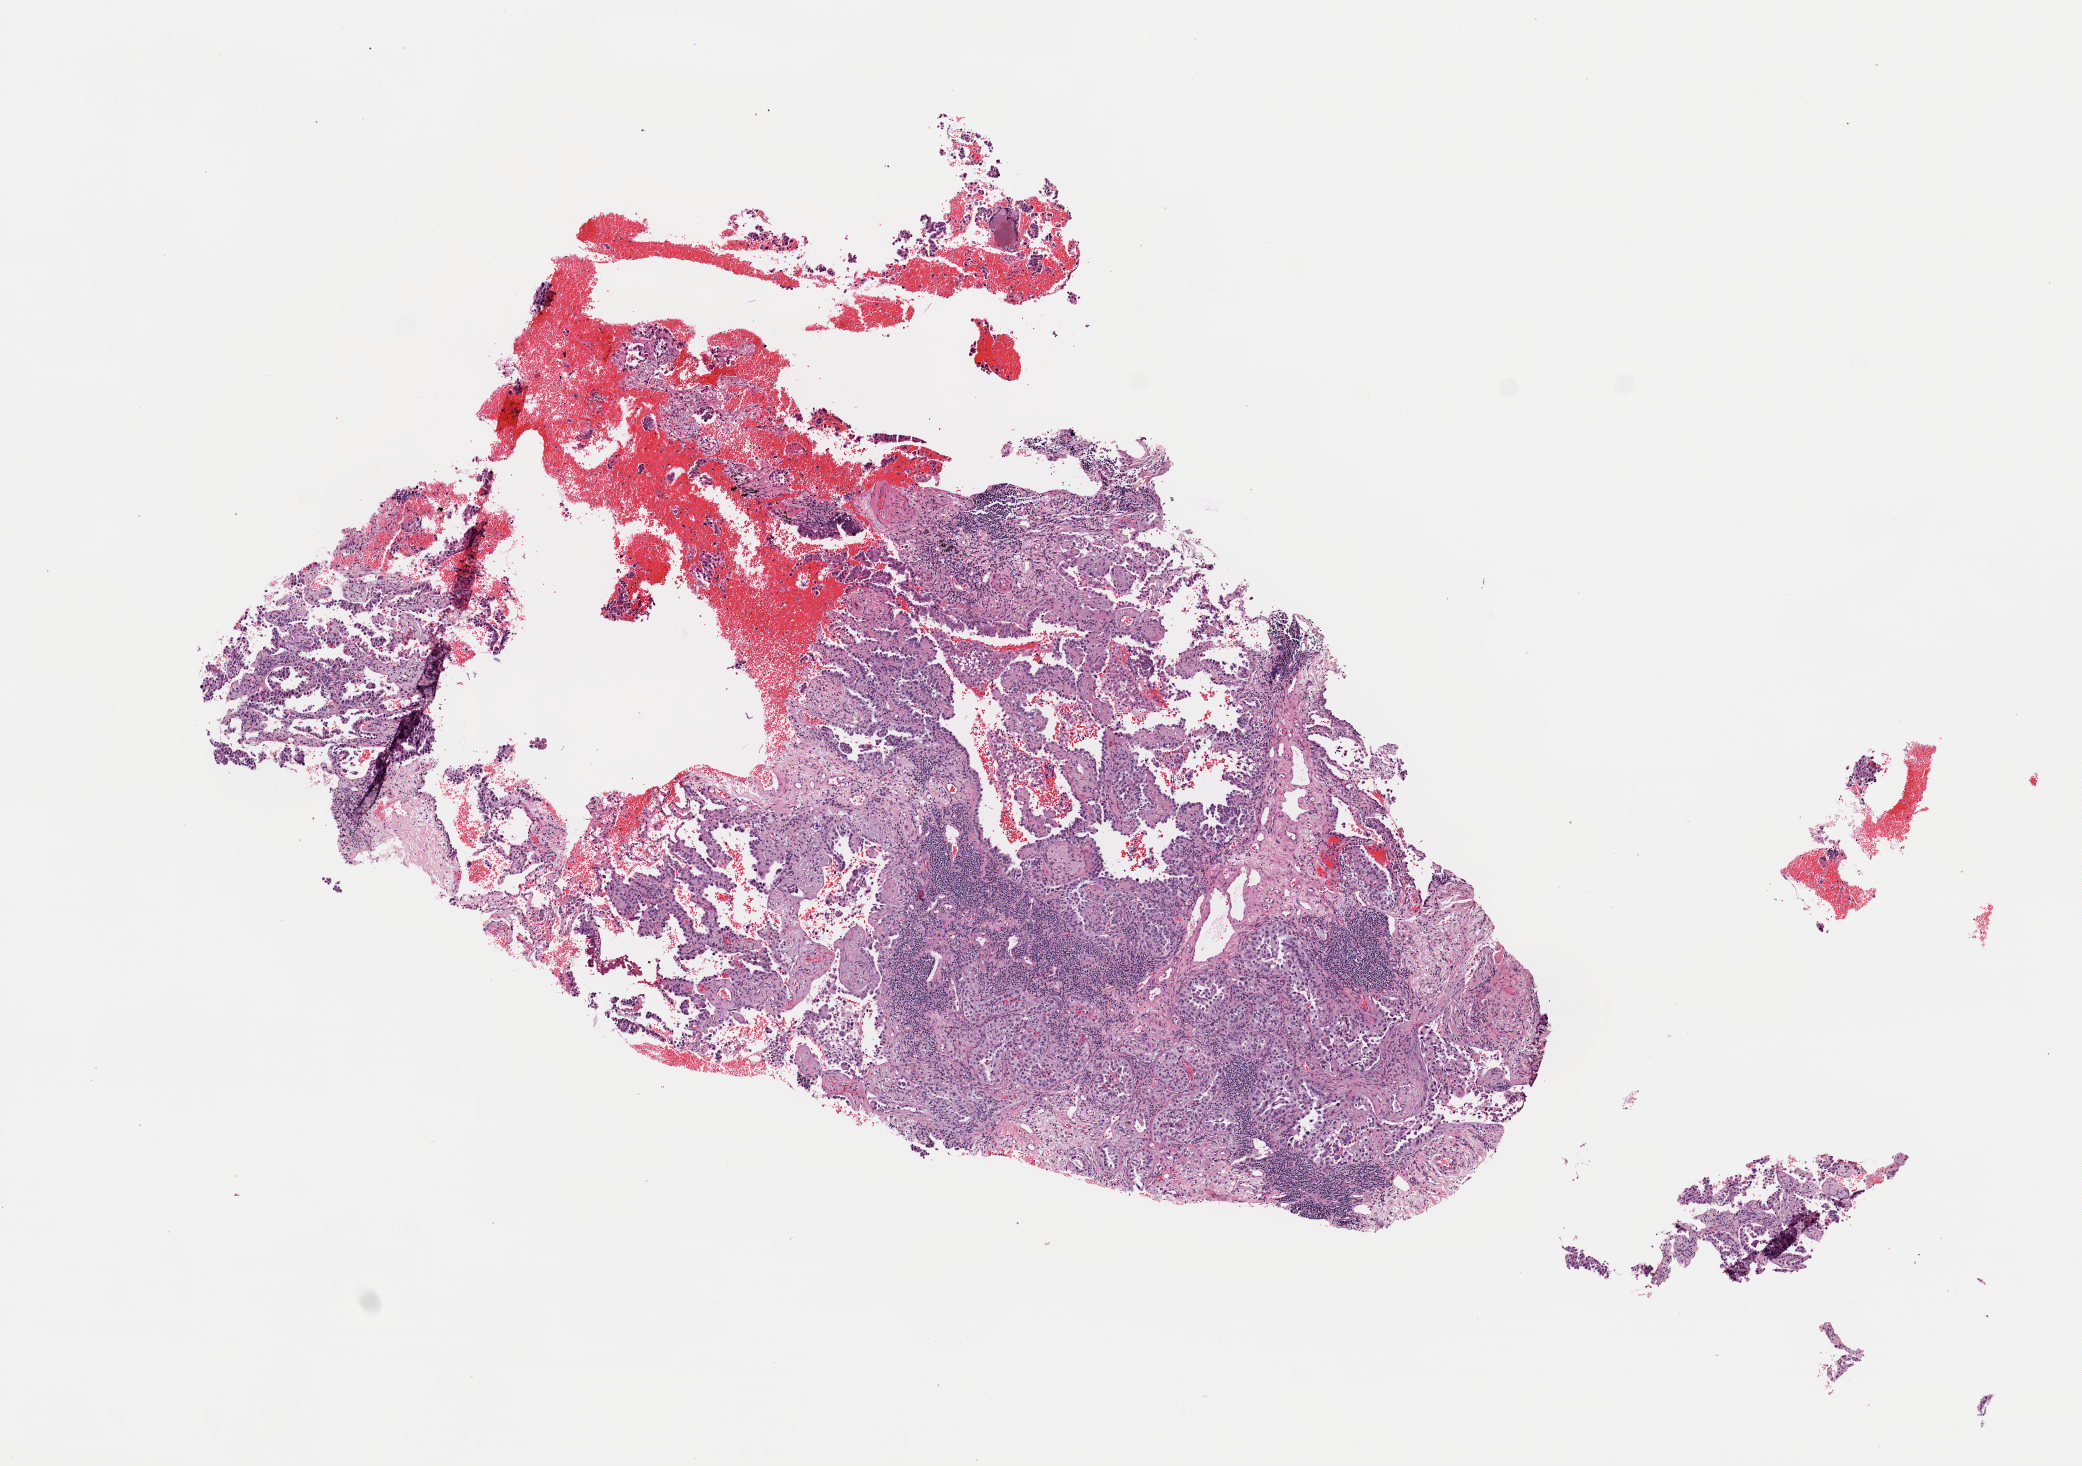
Hematoxylin and eosin (H&E) stained whole-slide image, shown as a low-resolution overview of the whole scanned area (about 8.2 x 5.8 mm, slide scanned at 40x); frozen section from the bottom of the tissue portion; primary tumour sample from the lung. Female, age 67 years at initial diagnosis. Pathologist review of this section (percent, as recorded): tumour cells 70%, tumour nuclei 80%, normal cells 0%, stromal cells 30%, necrosis 0%. Infiltration values recorded for this section: lymphocyte infiltration 25%, monocyte infiltration 2%, neutrophil infiltration 0%.
• diagnosis: Adenocarcinoma, NOS
• AJCC pathologic stage: IA (7th edition)